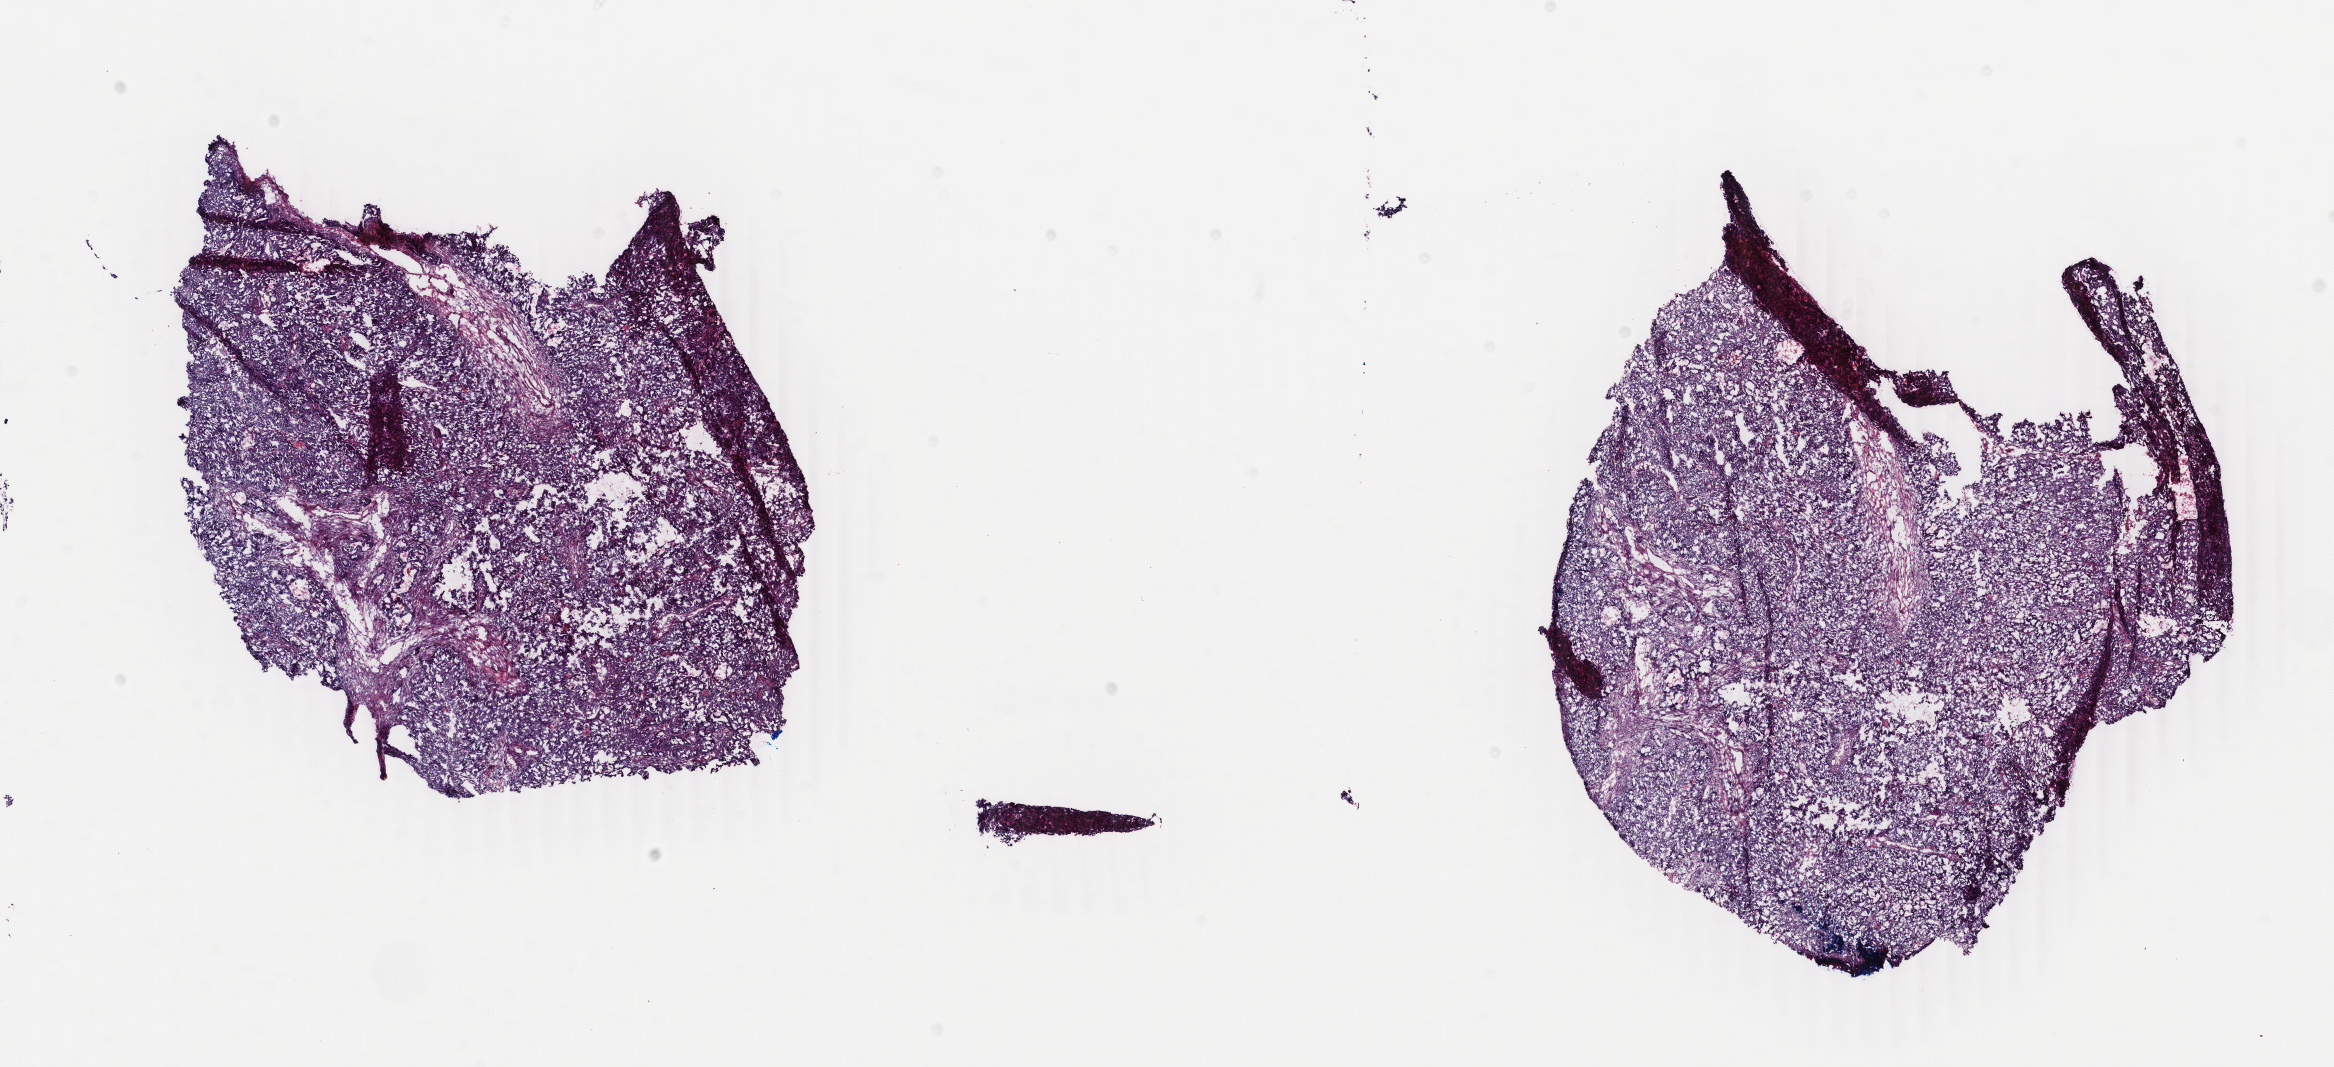
Digitized H&E tissue section (whole slide), a low-resolution overview of the entire scanned area, about 18.6 x 8.5 mm. Frozen section. Primary tumour sample from the uterus. Female, age 62 years at initial diagnosis. Pathologist review of this section (percent, as recorded): tumour cells 95%, tumour nuclei 80%.
Pathologic diagnosis: Endometrioid adenocarcinoma, NOS.